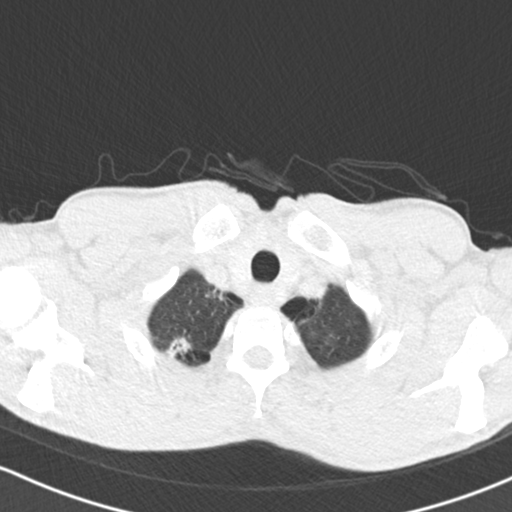
Low-dose screening chest CT, axial slice. First (baseline) screen. Lung window (W 1500 / L -600 HU). 2 mm slice thickness. Standard (soft-tissue) reconstruction kernel (B30f). 120 kVp. 512 × 512 image matrix, field of view 312 × 312 mm. Male, age 64 years at enrolment.
Lesion marked by an expert reader, bounding box [x1, y1, x2, y2] px = [149, 322, 202, 371]. Screening reader's record for this exam (one nodule recorded; not confirmed to be the boxed lesion): non-calcified nodule or mass ≥4 mm, right upper lobe, 13 × 11 mm, spiculated (stellate) margins, soft tissue attenuation. Official screen result: positive, change unspecified: nodule(s) >= 4 mm or enlarging nodule(s), mass(es), or other non-specific abnormalities suspicious for lung cancer.